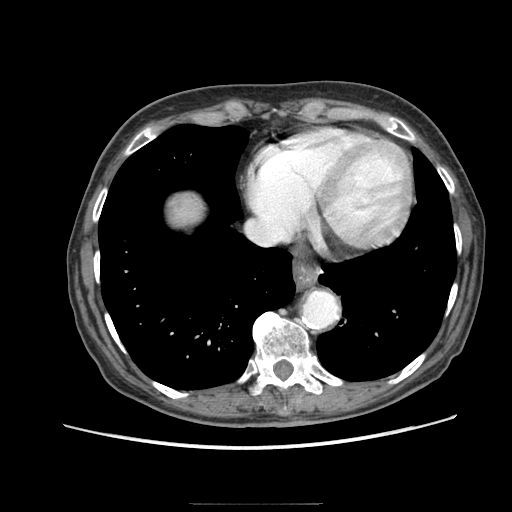
Contrast-enhanced abdominal CT (liver protocol), one axial slice. Position 78 of 83 along the scan axis. 140 kVp. Soft-tissue window (W 400 / L 40 HU). 512 × 512 image matrix. Case-level facts recorded for this patient, not image findings: diagnosis: hepatocellular carcinoma (patient treated with transarterial chemoembolisation; whether this scan precedes or follows treatment is not stated here); TNM stage (as recorded): Stage-I; Child-Pugh class: A; tumour differentiation: moderately differentiated; tumour nodularity: uninodular.
Outlined on this slice (semi-automatically segmented with operator editing):
- liver parenchyma outside the tumour (the mass and vessels are separate outlines, so this box may not span the whole liver): bounding box <170,196,202,224> (left, top, right, bottom; pixels)